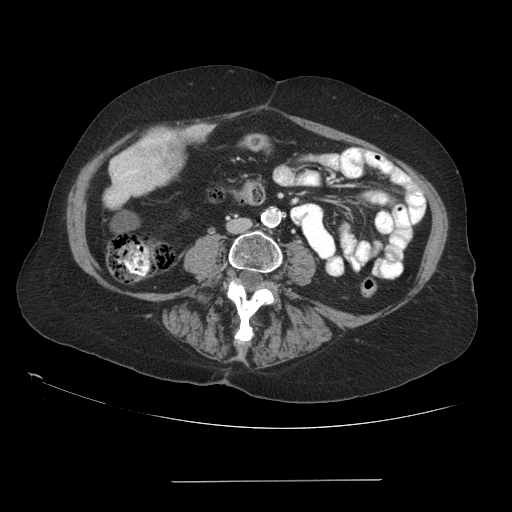
Contrast-enhanced abdominal CT (liver protocol), one axial slice; slice 14 of 89 in the series (ordered by position); reconstruction kernel STANDARD; soft-tissue window (W 400 / L 40 HU); 2.5 mm slice thickness; 512 × 512 image matrix. Case-level facts recorded for this patient, not image findings: diagnosis: hepatocellular carcinoma (patient treated with transarterial chemoembolisation; whether this scan precedes or follows treatment is not stated here); TNM stage (as recorded): Stage-IVA; Child-Pugh class: A; tumour differentiation: poorly differentiated; tumour nodularity: uninodular.
Annotated regions visible in this slice (semi-automatic segmentation, software-assisted and operator-edited):
- mass: box from (x=147, y=122) to (x=212, y=175) px